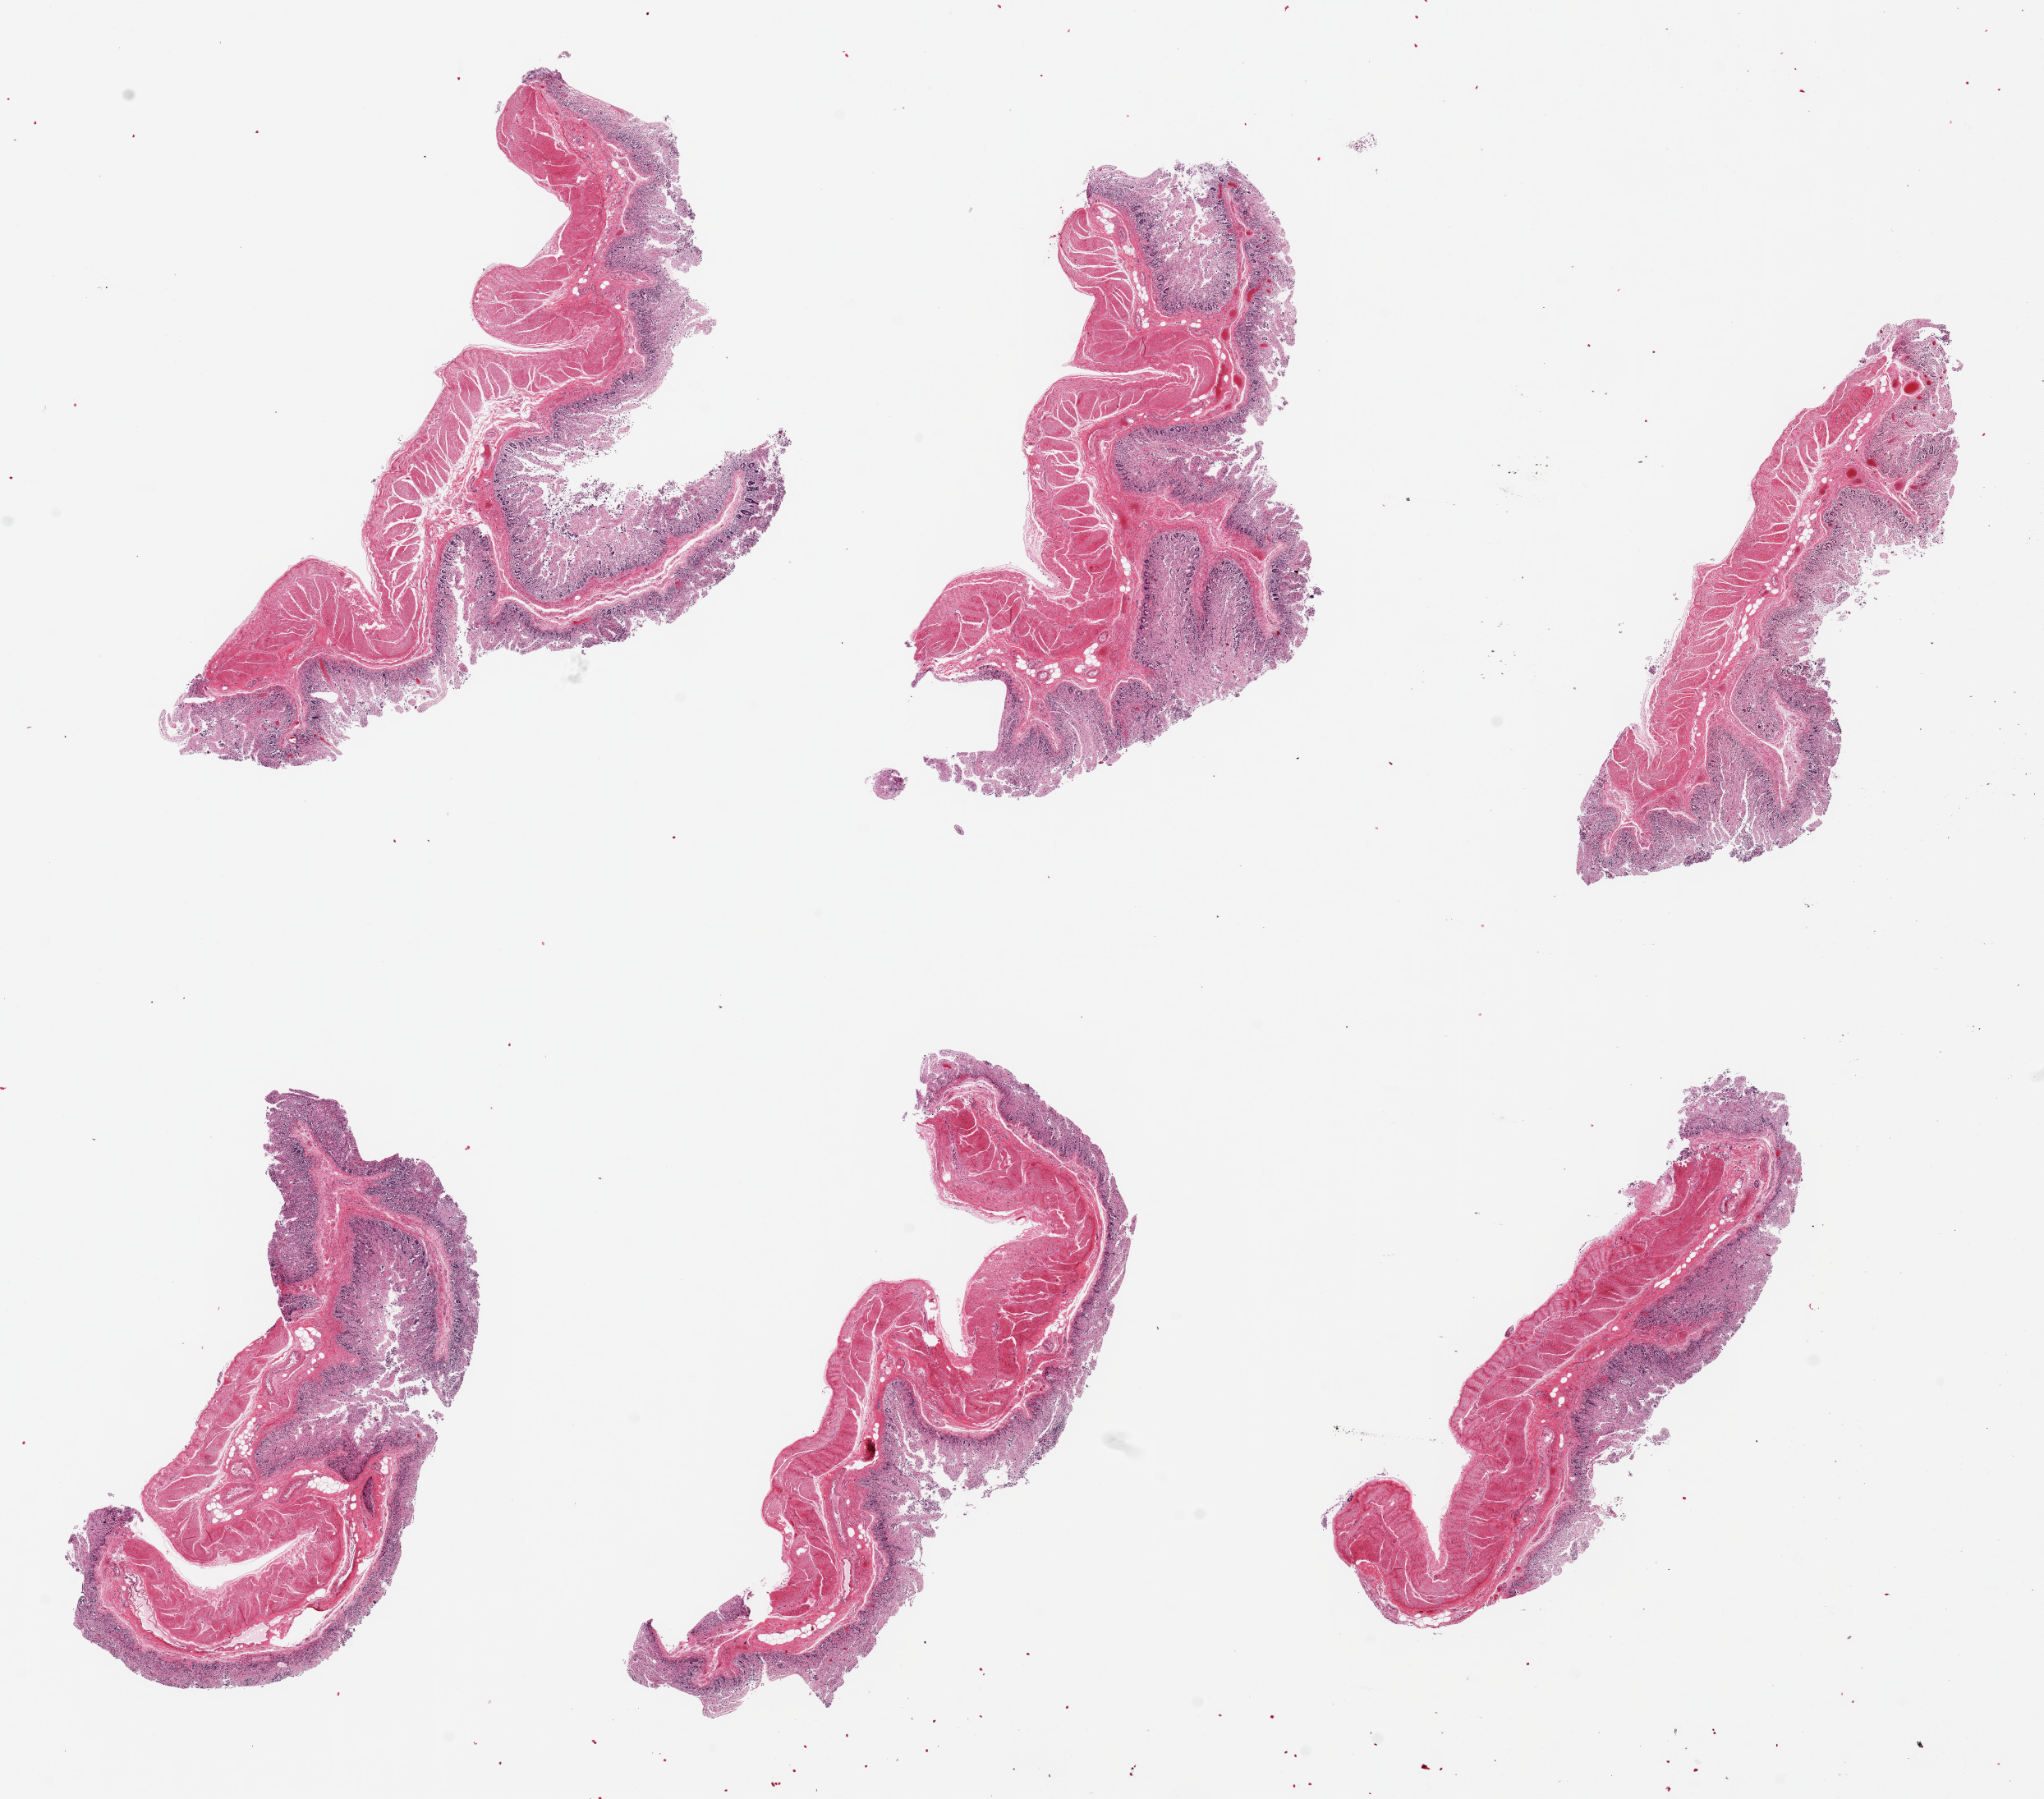
Digitized hematoxylin and eosin (H&E)-stained section, low-resolution overview of the scanned area, about 19.7 x 17.3 mm (acquisition: 20x scan), PAXgene-fixed, paraffin-embedded tissue, sampled site (target tissue): transverse colon, donor tissue sample.
Review note (as recorded): 6 pieces ~6x3mm. Mucosa badly autolyzed.